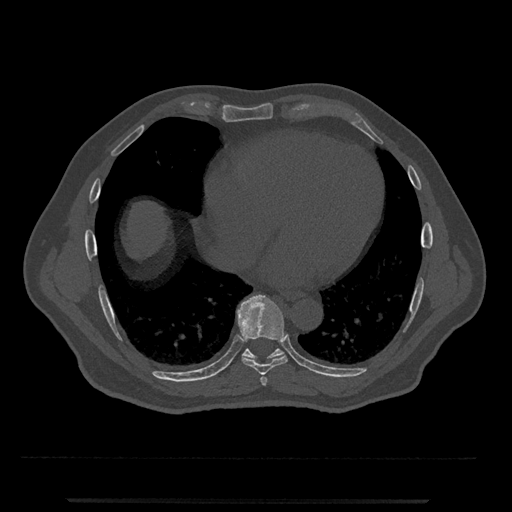
CT including the spine, one axial slice; slice 610 of 797 in the series (ordered by position); 120 kVp; bone window (W 1800 / L 400 HU); 512 × 512 image matrix, field of view 419 × 419 mm. Male patient, age 63 years. From the clinical record (not read from this slice): primary cancer: prostate.
Annotated regions visible in this slice (semi-automatic segmentation, software-assisted and operator-edited):
- T7 vertebra: bounding box (x1, y1, x2, y2) in pixels: (260, 375, 267, 386)
- T8 vertebra: (238, 295, 288, 375)
- T9 vertebra: (242, 348, 284, 362)